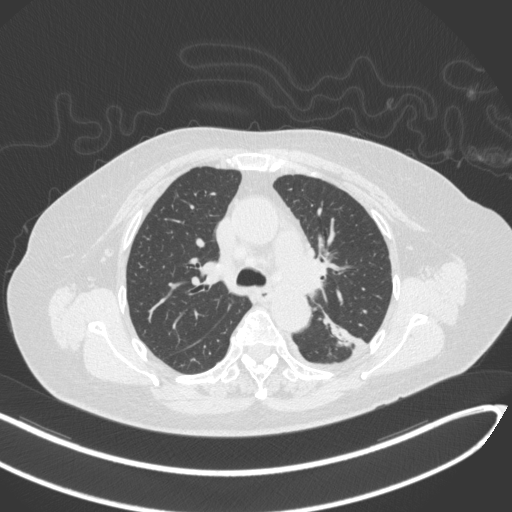
Chest CT, one axial slice; slice 210 of 270 in the series (ordered by position); lung window (W 1500 / L -600 HU); 512 × 512 image matrix. Patient: female, 76 years. From the clinical record (not read from this slice): clinical TNM (as recorded): T1c N0 M0.
Annotated regions visible in this slice (bounding box drawn by a radiologist):
- lung tumour (recorded histology: adenocarcinoma): bounding box [x1, y1, x2, y2] px = [320, 307, 355, 352]